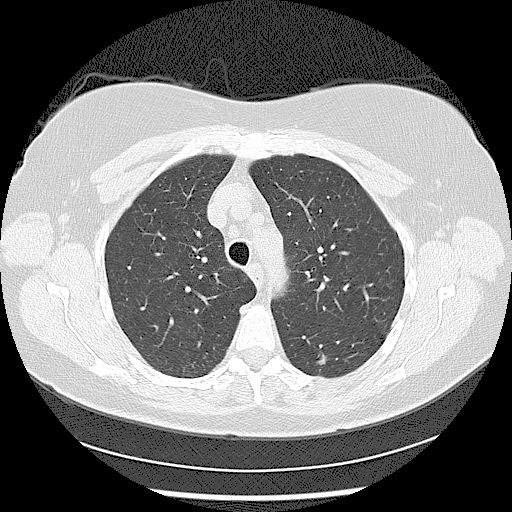
Axial slice from a low-dose chest CT screening exam. First (baseline) screen. Lung window (W 1500 / L -600 HU). 2.5 mm slice thickness. Lung (sharp) reconstruction kernel (LUNG). 120 kVp. Female, age 56 years at enrolment. Current smoker at enrolment.
Expert reader's lesion annotation, bounding box <292,338,343,394> (left, top, right, bottom; pixels). The screening reader recorded 2 non-calcified nodules or masses ≥4 mm on this exam (left lower lobe, left lower lobe); which of them this box marks is not recorded. Later outcome: lung cancer diagnosed 638 days after this screen — adenocarcinoma, NOS, left lower lobe, moderately differentiated (G2), stage IIA (AJCC 6th edition), 15 mm at pathology.